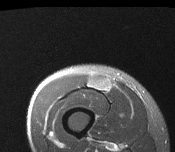
MRI of an extremity soft-tissue mass, one axial slice. Slice 34 of 116 in the series (ordered by position). T2-weighted fat-saturated. MR volume resampled by the dataset authors to the PET/CT grid (not the native acquisition matrix). 3.27 mm slice thickness. 175 × 152 image matrix, field of view 171 × 148 mm. Male patient. Case-level facts recorded for this patient, not image findings: histological type: pleiomorphic leiomyosarcoma; grade: intermediate; site of the primary tumour: right thigh.
Structures marked on this image (expert contour drawn on MRI and transferred to this co-registered scan by the dataset authors):
- gross tumour volume including surrounding oedema: box from (x=86, y=74) to (x=112, y=93) px